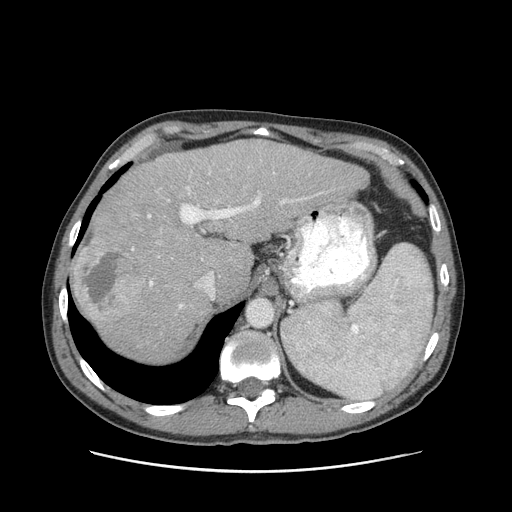
Contrast-enhanced abdominal CT (liver protocol), one axial slice. Slice 71 of 93 in the series (ordered by position). Reconstruction kernel STANDARD. 120 kVp. Soft-tissue window (W 400 / L 40 HU). 2.5 mm slice thickness. 512 × 512 image matrix, field of view 380 × 380 mm. From the clinical record (not read from this slice): diagnosis: hepatocellular carcinoma (patient treated with transarterial chemoembolisation; whether this scan precedes or follows treatment is not stated here); TNM stage (as recorded): Stage-II; Child-Pugh class: A; tumour nodularity: multinodular; tumour size: 1 cm.
Annotated regions visible in this slice (semi-automatic segmentation, software-assisted and operator-edited):
- abdominal aorta: box from (x=247, y=299) to (x=272, y=325) px
- liver parenchyma outside the tumour (the mass and vessels are separate outlines, so this box may not span the whole liver): (x=72, y=140)–(x=368, y=360)
- mass: (x=74, y=246)–(x=142, y=322)
- liver vessels: (x=132, y=186)–(x=299, y=309)